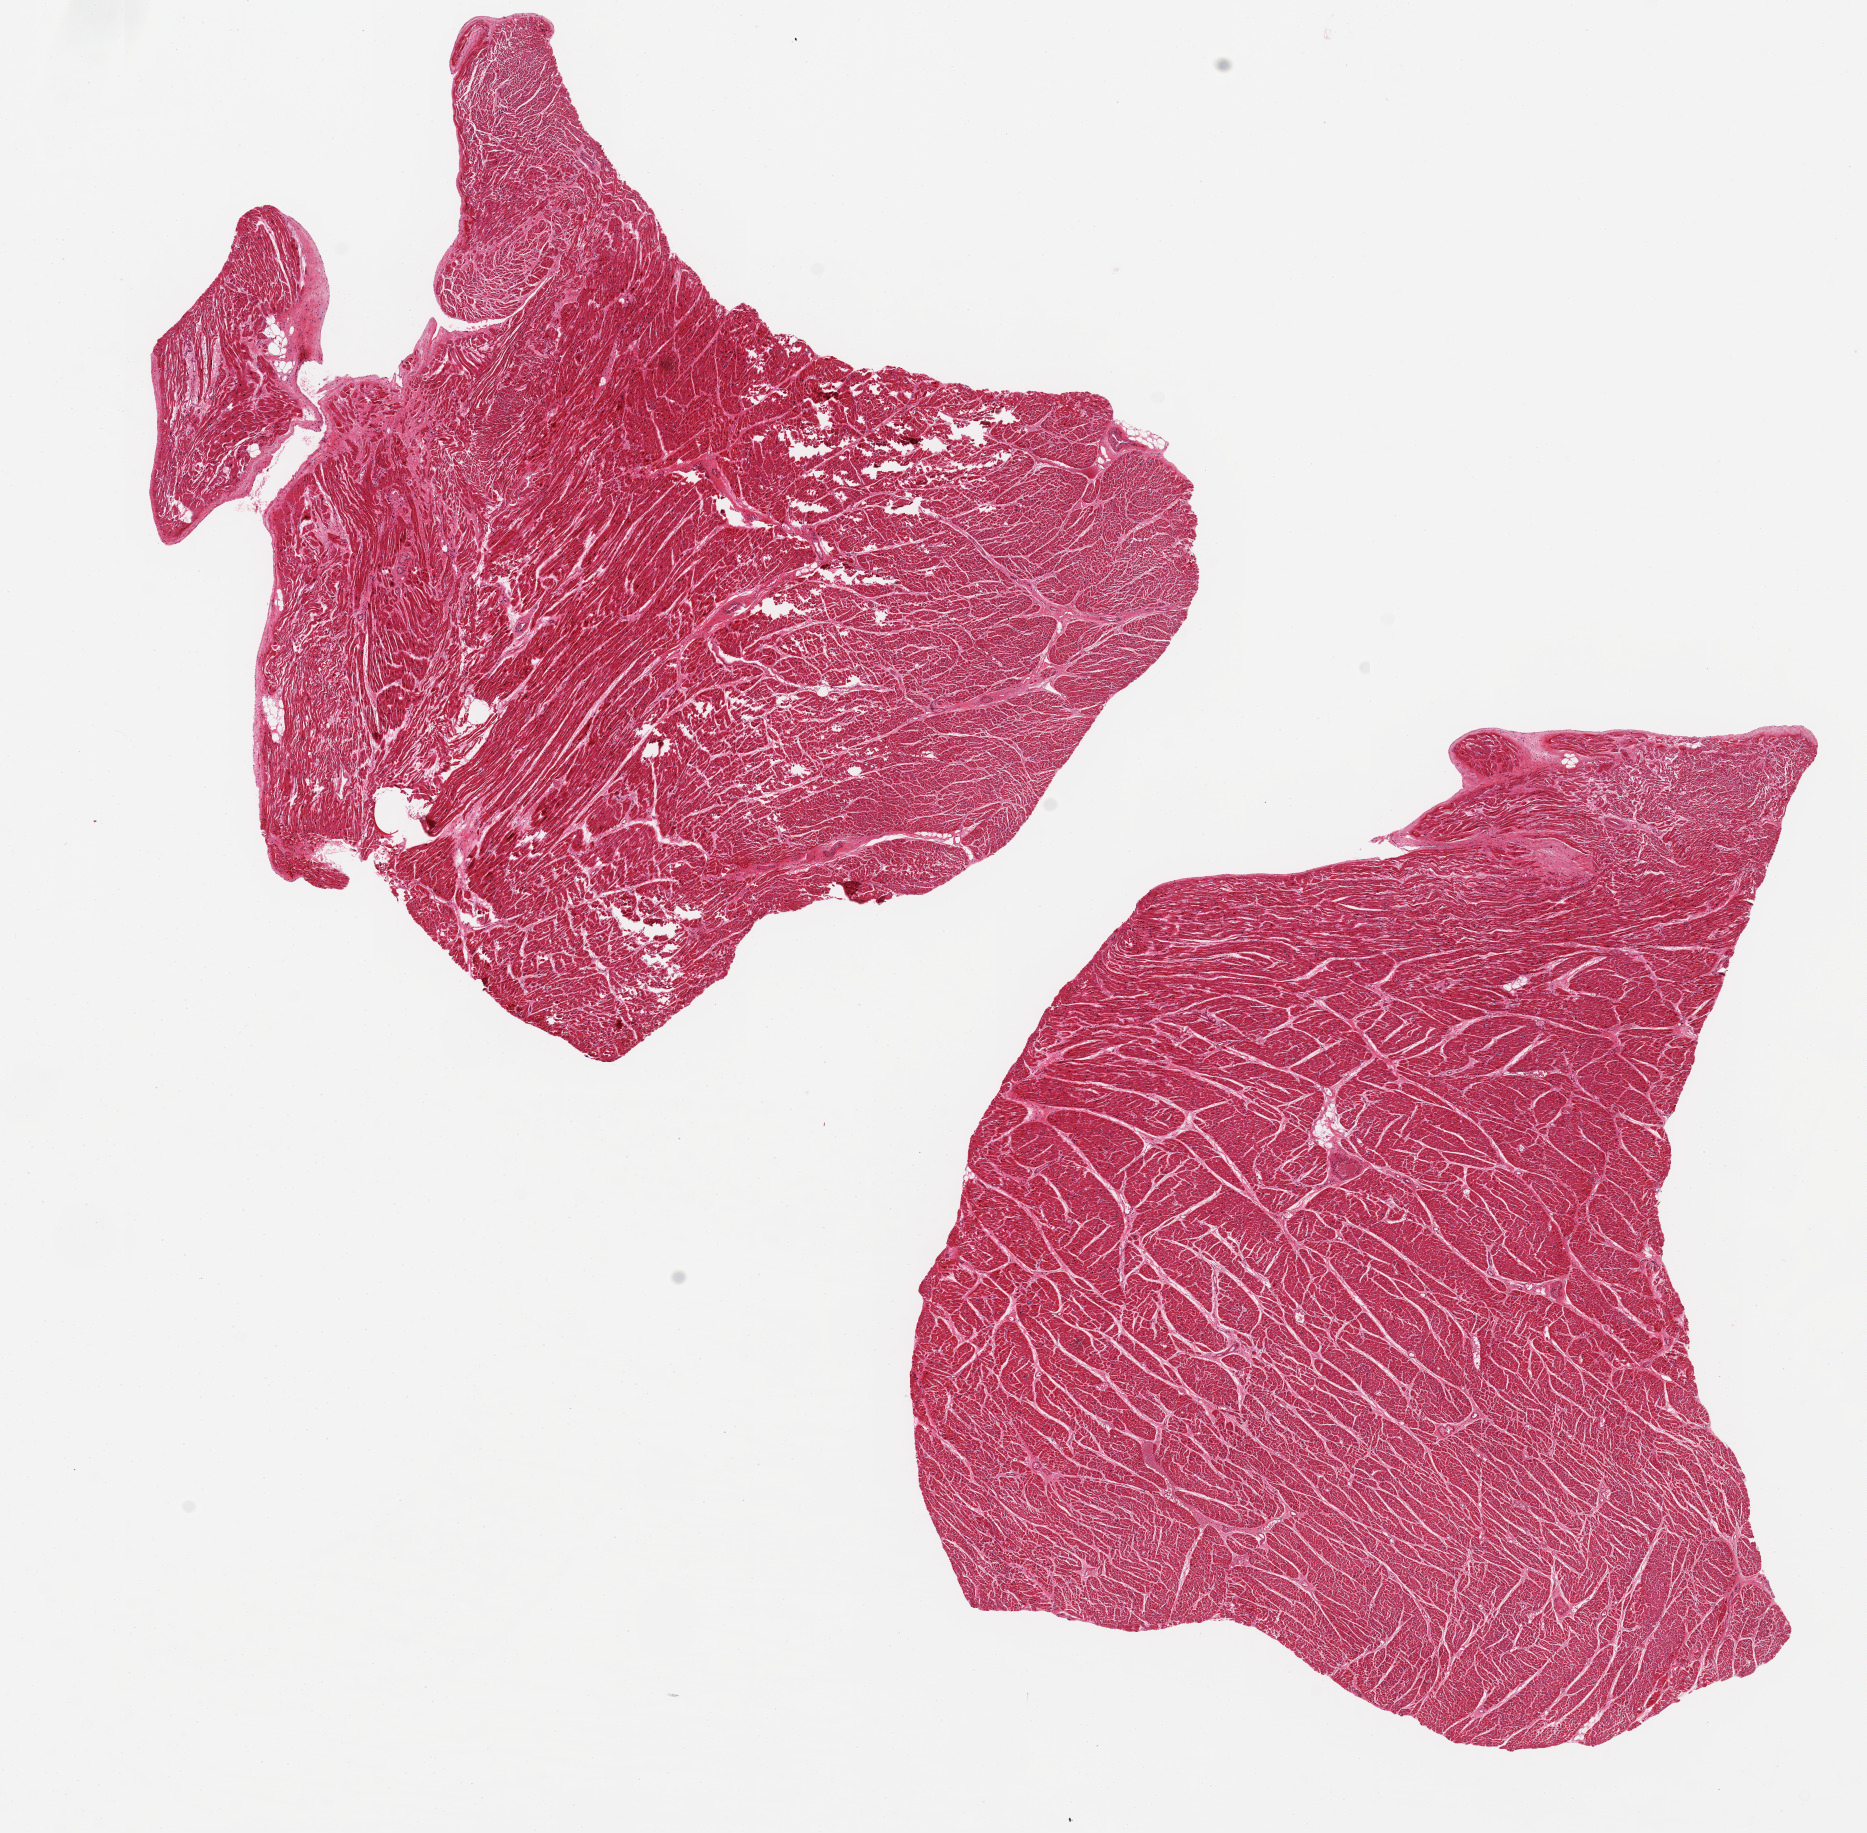
Hematoxylin and eosin (H&E) whole-slide image — low-resolution overview of the scanned area, about 14.8 x 14.5 mm (slide scanned at 20x), PAXgene-fixed paraffin-embedded (PFPE) section, sampled site (target tissue): heart, donor tissue sample. Donor: male.
Reviewer comment on this tissue sample: 2 ~8x6.5mm aliquots. Mild ischemic changes. Minute (0.7x0.3mm) fibrous scar).